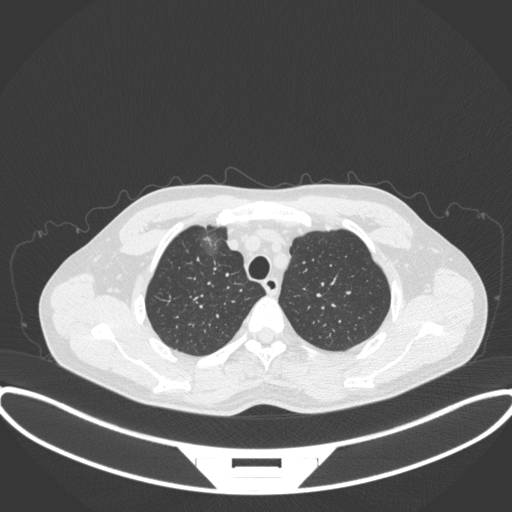
Chest CT, one axial slice. Position 299 of 395 along the scan axis. 120 kVp. Lung window (W 1500 / L -600 HU). 1 mm slice thickness. 512 × 512 image matrix, field of view 424 × 424 mm. Male patient, age 60 years. Case-level facts recorded for this patient, not image findings: clinical TNM (as recorded): T1c N0 M0.
Annotated regions visible in this slice (rectangle marked by the reading radiologist):
- lung tumour (recorded histology: adenocarcinoma): bounding box [x1, y1, x2, y2] px = [201, 231, 224, 261]